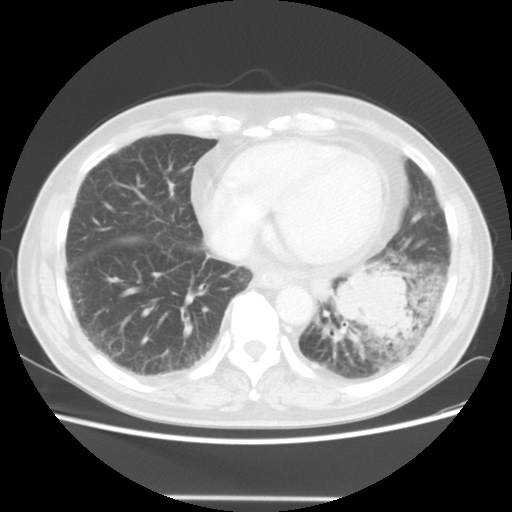
Chest CT, one axial slice. Position 15 of 56 along the scan axis. Reconstruction kernel STANDARD. Lung window (W 1500 / L -600 HU). 5 mm slice thickness. 512 × 512 image matrix. Male patient, age 66 years. Case-level facts recorded for this patient, not image findings: clinical TNM (as recorded): T4 N3 M0; histopathological grade: G3.
Structures marked on this image (bounding box drawn by a radiologist):
- lung tumour (recorded histology: small cell carcinoma): bounding box (x1, y1, x2, y2) in pixels: (332, 265, 420, 345)